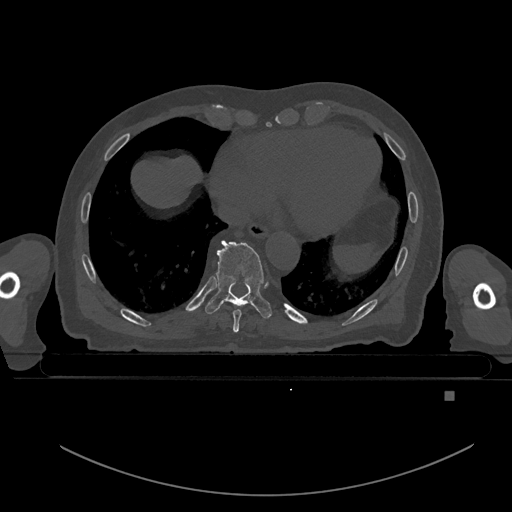
CT including the spine, one axial slice. Slice 159 of 969 in the series (ordered by position). Bone window (W 1800 / L 400 HU). 0.5 mm slice thickness. 512 × 512 image matrix, field of view 456 × 456 mm. Male patient, age 82 years. From the clinical record (not read from this slice): primary cancer: prostate.
Annotated regions visible in this slice (semi-automatic segmentation, software-assisted and operator-edited):
- T8 vertebra: bounding box <232,298,242,333> (left, top, right, bottom; pixels)
- T9 vertebra: <205,240,272,319>